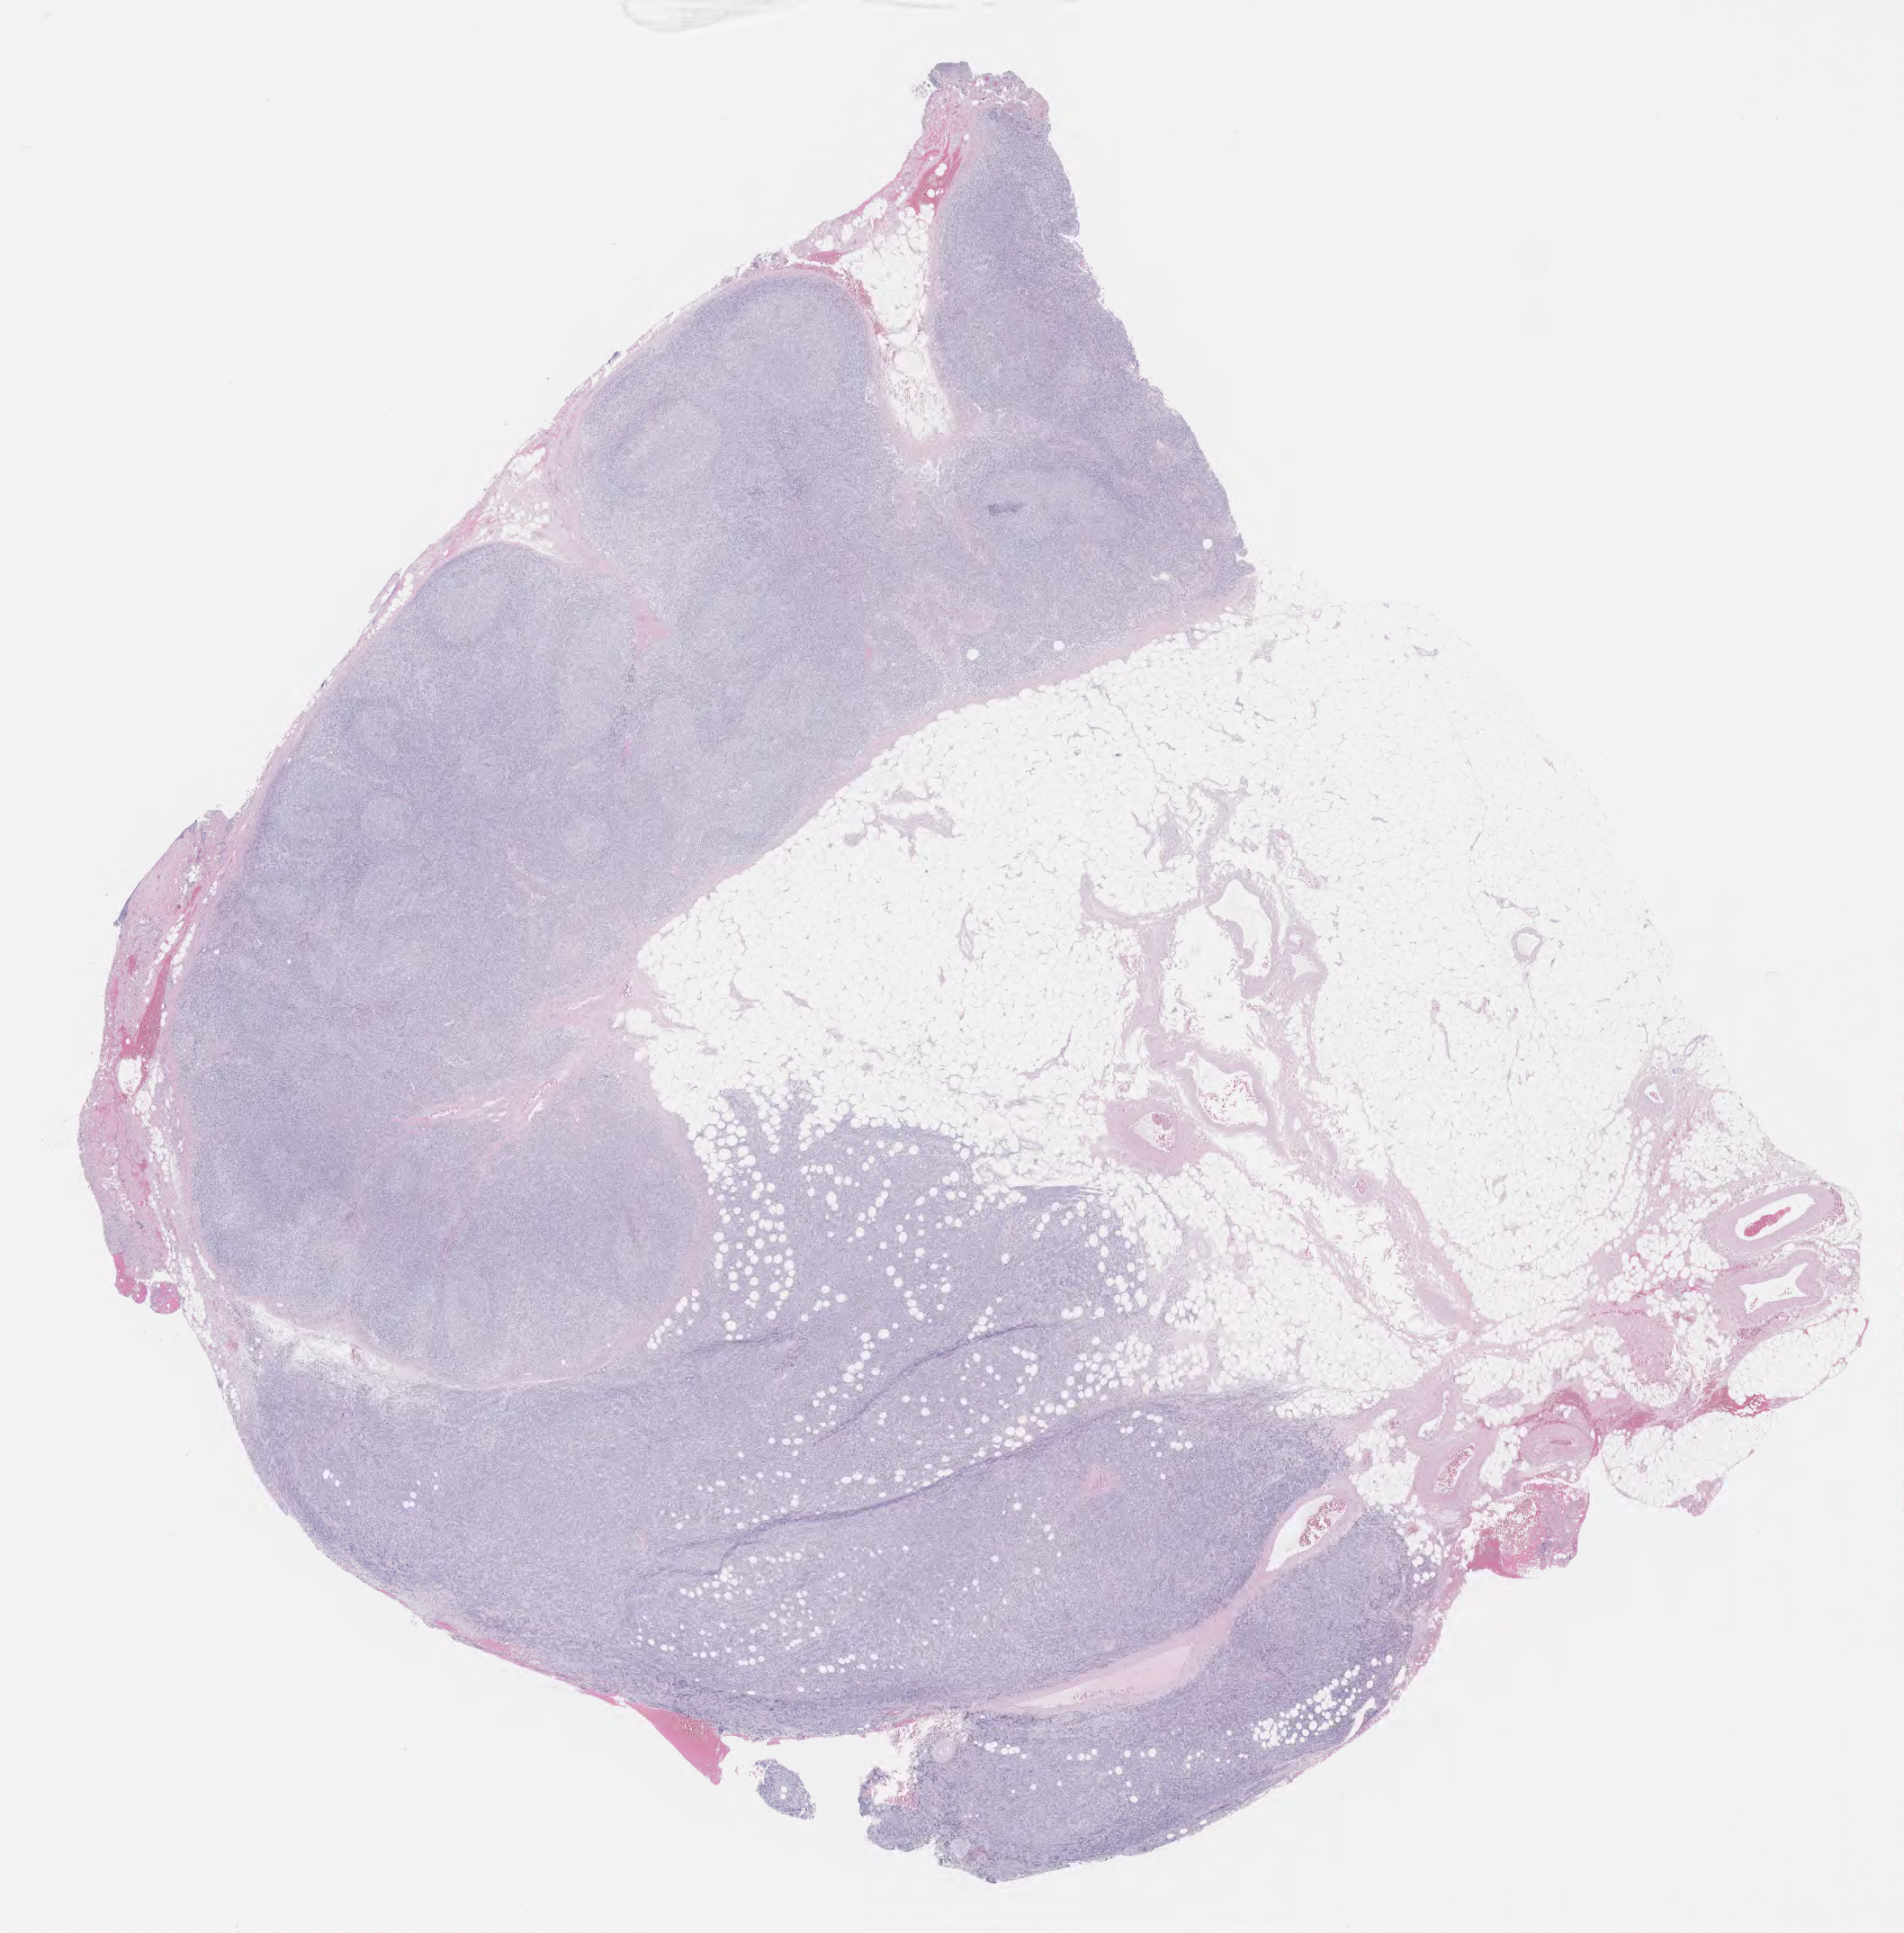
Whole-slide image, hematoxylin and eosin (H&E) stain, low-resolution overview of the scanned area, about 17.1 x 17.4 mm. Specimen: tumor tissue. Site: upper limb lymph node. Male patient, aged 28.
Diagnosis: Burkitt lymphoma, NOS.